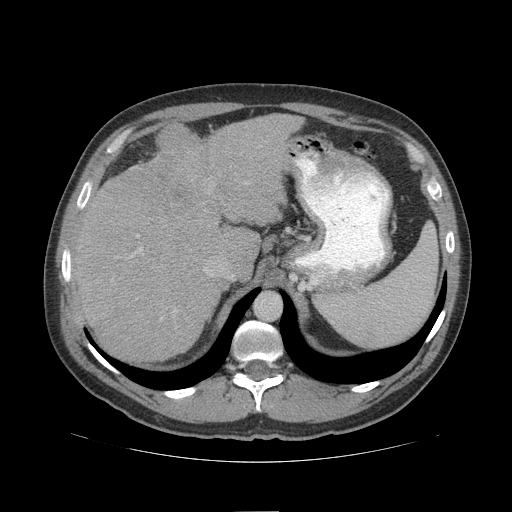
Contrast-enhanced abdominal CT (liver protocol), one axial slice; position 74 of 109 along the scan axis; reconstruction kernel STANDARD; soft-tissue window (W 400 / L 40 HU); 2.5 mm slice thickness; 512 × 512 image matrix. Case-level facts recorded for this patient, not image findings: diagnosis: hepatocellular carcinoma (patient treated with transarterial chemoembolisation; whether this scan precedes or follows treatment is not stated here); TNM stage (as recorded): Stage-IIIB; Child-Pugh class: A; tumour differentiation: poorly differentiated; tumour nodularity: multinodular.
Outlined on this slice (semi-automatically segmented with operator editing):
- liver parenchyma outside the tumour (the mass and vessels are separate outlines, so this box may not span the whole liver): bounding box <72,114,302,362> (left, top, right, bottom; pixels)
- mass: <153,122,230,222>
- liver vessels: <140,248,142,251>